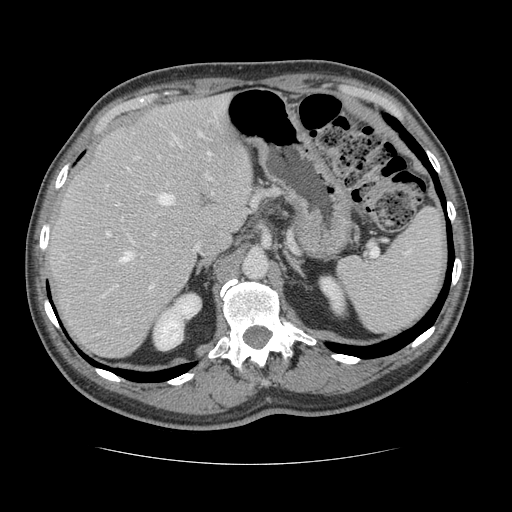
Contrast-enhanced abdominal CT, one axial slice; slice 89 of 134 in the series (ordered by position); reconstruction kernel STANDARD; 120 kVp; soft-tissue window (W 400 / L 40 HU); 2.5 mm slice thickness; 512 × 512 image matrix, field of view 377 × 377 mm. Male patient, age 68 years. From the clinical record (not read from this slice): diagnosis: colorectal cancer liver metastases, imaged before liver resection; multiple liver metastases: yes; largest metastasis: 2.2 cm; disease in both lobes: no.
Annotated regions visible in this slice (outlined manually by an expert reader):
- hepatic veins: bounding box <120,138,213,263> (left, top, right, bottom; pixels)
- liver: <47,97,252,358>
- planned liver remnant (the part of the liver to remain after resection): <48,97,252,337>
- portal vein (with intrahepatic branches): <106,132,214,289>